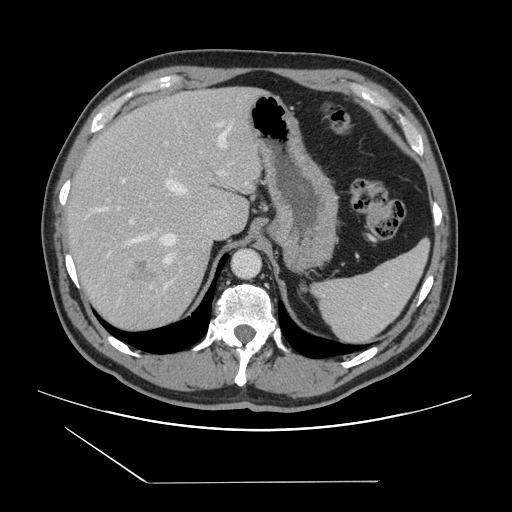
Contrast-enhanced abdominal CT, one axial slice. Slice 108 of 157 in the series (ordered by position). 120 kVp. Intravenous contrast given. Soft-tissue window (W 400 / L 40 HU). 2.5 mm slice thickness. 512 × 512 image matrix. Male patient, age 61 years. From the clinical record (not read from this slice): diagnosis: colorectal cancer liver metastases, imaged before liver resection; multiple liver metastases: yes; largest metastasis: 5.5 cm; disease in both lobes: yes.
Annotated regions visible in this slice (outlined manually by an expert reader):
- hepatic veins: bounding box (x1, y1, x2, y2) in pixels: (97, 124, 232, 266)
- liver: (63, 88, 260, 332)
- planned liver remnant (the part of the liver to remain after resection): (66, 88, 237, 230)
- portal vein (with intrahepatic branches): (122, 141, 226, 286)
- liver metastasis: (126, 257, 175, 308)